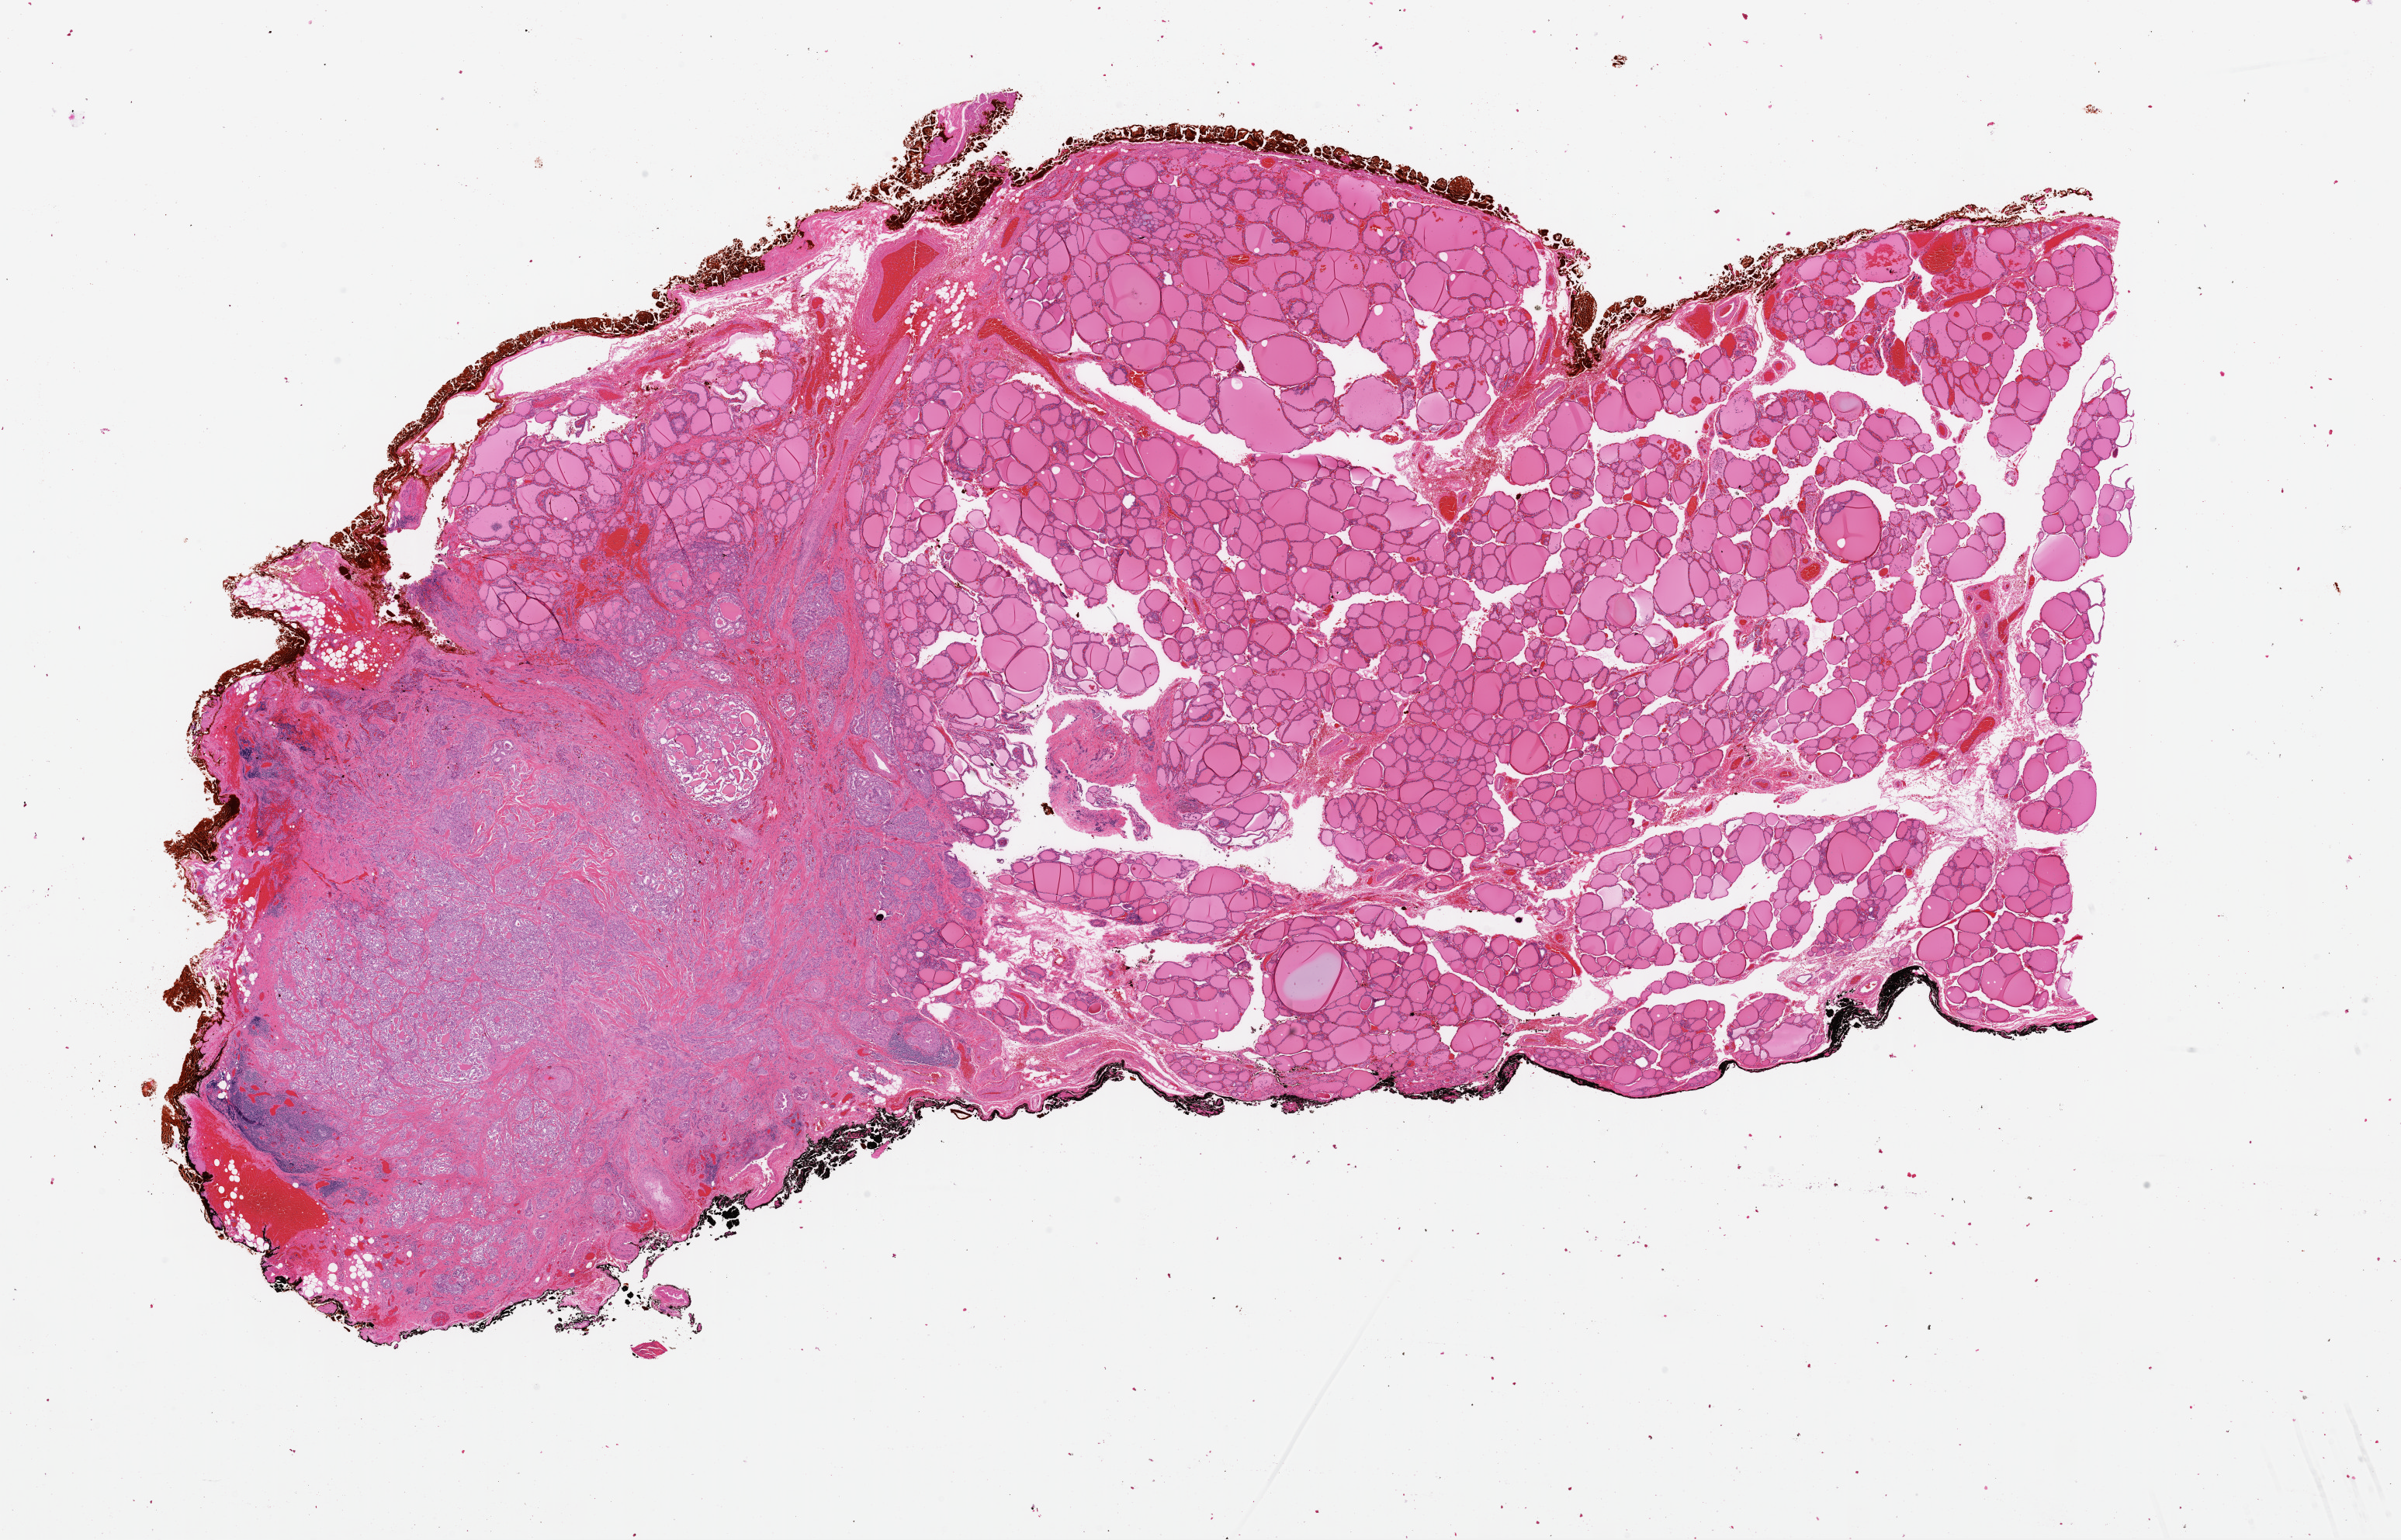
Whole-slide histology image, Hematoxylin and eosin (H&E) stained — low-resolution overview of the scanned area, about 24.4 x 15.7 mm (slide scanned at 40x); formalin-fixed paraffin-embedded (FFPE) diagnostic section; primary tumour sample from the thyroid. Female, age 27 years at initial diagnosis.
- lymph nodes positive (case pathology): 0 of 2 examined
- pathologic diagnosis: Papillary adenocarcinoma, NOS (thyroid gland)
- laterality: left
- AJCC pathologic stage: I